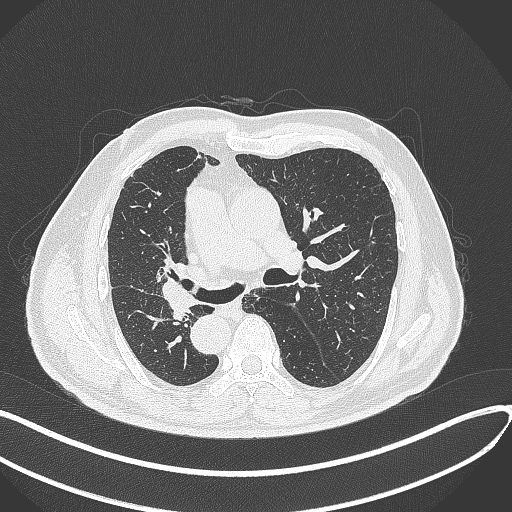
Chest CT, one axial slice; lung window (W 1500 / L -600 HU); 512 × 512 image matrix, field of view 400 × 400 mm. Male patient, age 67 years. From the clinical record (not read from this slice): clinical TNM (as recorded): T2a N0 M0.
Structures marked on this image (bounding box drawn by a radiologist):
- lung tumour (recorded histology: squamous cell carcinoma): bounding box [x1, y1, x2, y2] px = [157, 275, 198, 325]